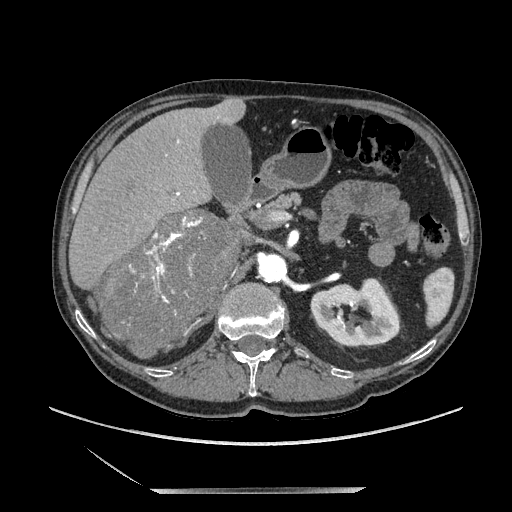
Contrast-enhanced abdominal CT, one axial slice; slice 118 of 243 in the series (ordered by position); soft-tissue window (W 400 / L 40 HU); 512 × 512 image matrix, field of view 420 × 420 mm. Male patient. From the clinical record (not read from this slice): diagnosis: adrenocortical carcinoma; tumour side: right adrenal; tumour size at pathology: 16 cm; Ki-67 index: 17 %.
Outlined on this slice (semi-automatic segmentation, software-assisted and operator-edited):
- mass: box from (x=102, y=210) to (x=235, y=356) px